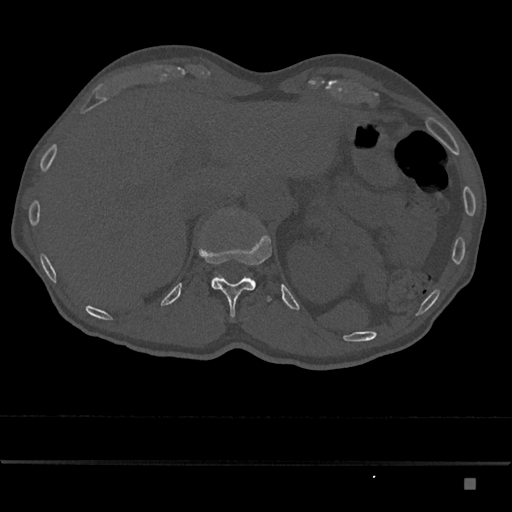
CT including the spine, one axial slice. Slice 601 of 797 in the series (ordered by position). 120 kVp. Bone window (W 1800 / L 400 HU). 0.5 mm slice thickness. 512 × 512 image matrix, field of view 390 × 390 mm. Male patient, age 72 years. From the clinical record (not read from this slice): primary cancer: prostate.
Annotated regions visible in this slice (semi-automatic segmentation, software-assisted and operator-edited):
- L1 vertebra: bounding box <211,209,235,282> (left, top, right, bottom; pixels)
- T12 vertebra: <199,235,272,318>